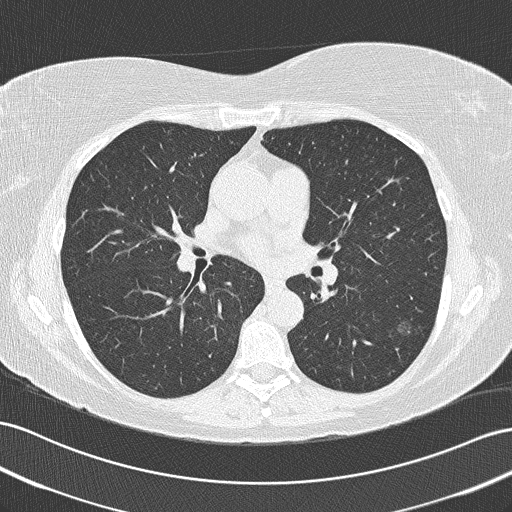
Axial slice from a low-dose chest CT screening exam; first (baseline) screen; lung window (W 1500 / L -600 HU); lung (sharp) reconstruction kernel (B50f); slice 83 of 172 in the series; 512 × 512 image matrix. Female, age 57 years at enrolment. Current smoker at enrolment.
- Expert-annotated lung lesion, box from (x=384, y=310) to (x=430, y=351) px.
- Reader record for this screening exam (exam-level; its link to the box is not recorded): non-calcified nodule or mass ≥4 mm, left lower lobe, 11 × 11 mm, spiculated (stellate) margins, ground glass attenuation.
- Lung cancer was diagnosed 849 days after this screen: bronchiolo-alveolar adenocarcinoma, NOS, left lower lobe, well differentiated (G1), stage IA (AJCC 6th edition), 16 mm at pathology.